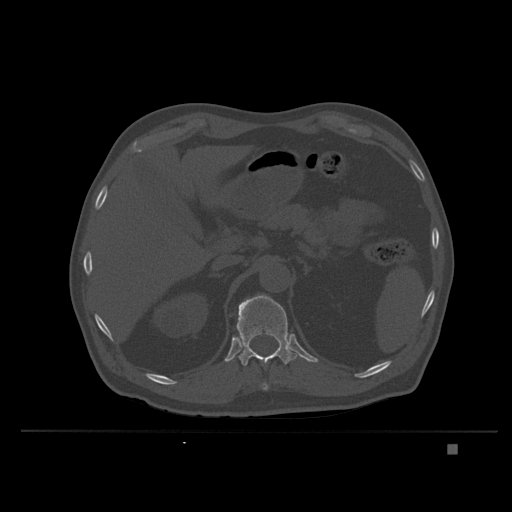
CT including the spine, one axial slice. Position 161 of 435 along the scan axis. Bone window (W 1800 / L 400 HU). 512 × 512 image matrix, field of view 434 × 434 mm. Male patient, age 73 years. Case-level facts recorded for this patient, not image findings: primary cancer: skin.
Structures marked on this image (semi-automatically segmented with operator editing):
- T11 vertebra: bounding box [x1, y1, x2, y2] px = [261, 383, 269, 391]
- T12 vertebra: [230, 295, 297, 366]